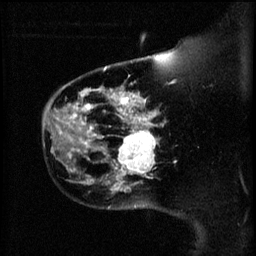
Breast MRI (dynamic contrast-enhanced), one sagittal slice. Position 46 of 60 along the scan axis. 3 images stored at this slice position (order not interpretable as contrast timing). 1.5 T. TE 4.2 ms, TR 11 ms. 2 mm slice thickness. 256 × 256 image matrix, field of view 180 × 180 mm. Female patient, age 44 years.
Annotated regions visible in this slice (semi-automatically segmented with operator editing):
- analysis volume of interest (the breast-tissue region the enhancement analysis was run in; not a lesion): bounding box (x1, y1, x2, y2) in pixels: (110, 124, 161, 179)
- tumour enhancement mask (voxels above the 70 % enhancement threshold inside the analysis volume of interest): (116, 124, 157, 179)